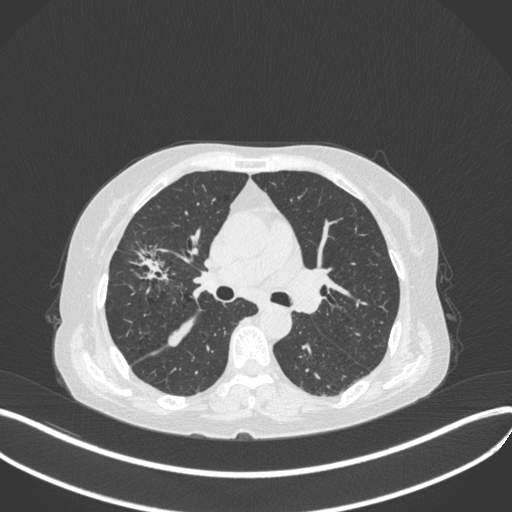
Chest CT, one axial slice; position 238 of 429 along the scan axis; reconstruction kernel B31f; lung window (W 1500 / L -600 HU); 512 × 512 image matrix, field of view 400 × 400 mm. Patient: female, 69 years. Case-level facts recorded for this patient, not image findings: clinical TNM (as recorded): T1b N3 M0.
Annotated regions visible in this slice (bounding box drawn by a radiologist):
- lung tumour (recorded histology: small cell carcinoma): bounding box <124,236,176,291> (left, top, right, bottom; pixels)